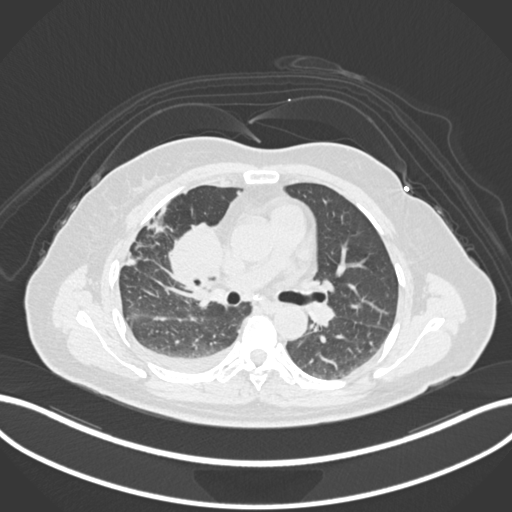
Chest CT, one axial slice. Slice 82 of 172 in the series (ordered by position). Reconstruction kernel B30f. 120 kVp. Lung window (W 1500 / L -600 HU). 512 × 512 image matrix. Patient: female, 52 years. From the clinical record (not read from this slice): clinical TNM (as recorded): T3 N1 M1.
Structures marked on this image (bounding box drawn by a radiologist):
- lung tumour (recorded histology: adenocarcinoma): bounding box (x1, y1, x2, y2) in pixels: (165, 218, 224, 287)